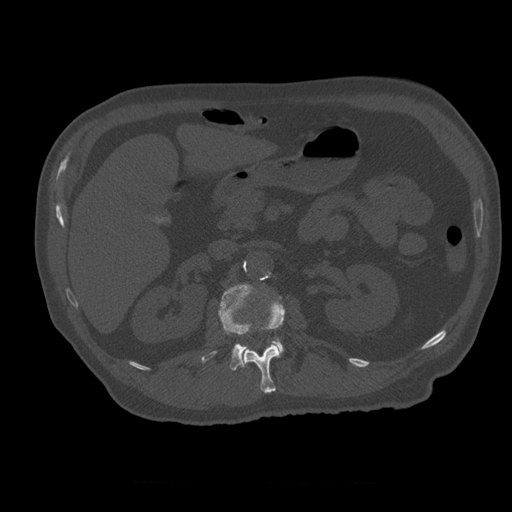
CT including the spine, one axial slice. Position 228 of 399 along the scan axis. Reconstruction kernel STANDARD. Bone window (W 1800 / L 400 HU). 512 × 512 image matrix, field of view 407 × 407 mm. Patient age 73 years. Case-level facts recorded for this patient, not image findings: primary cancer: prostate.
Annotated regions visible in this slice (semi-automatic segmentation, software-assisted and operator-edited):
- L1 vertebra: box from (x=242, y=297) to (x=285, y=394) px
- L2 vertebra: (x=202, y=284)–(x=284, y=371)